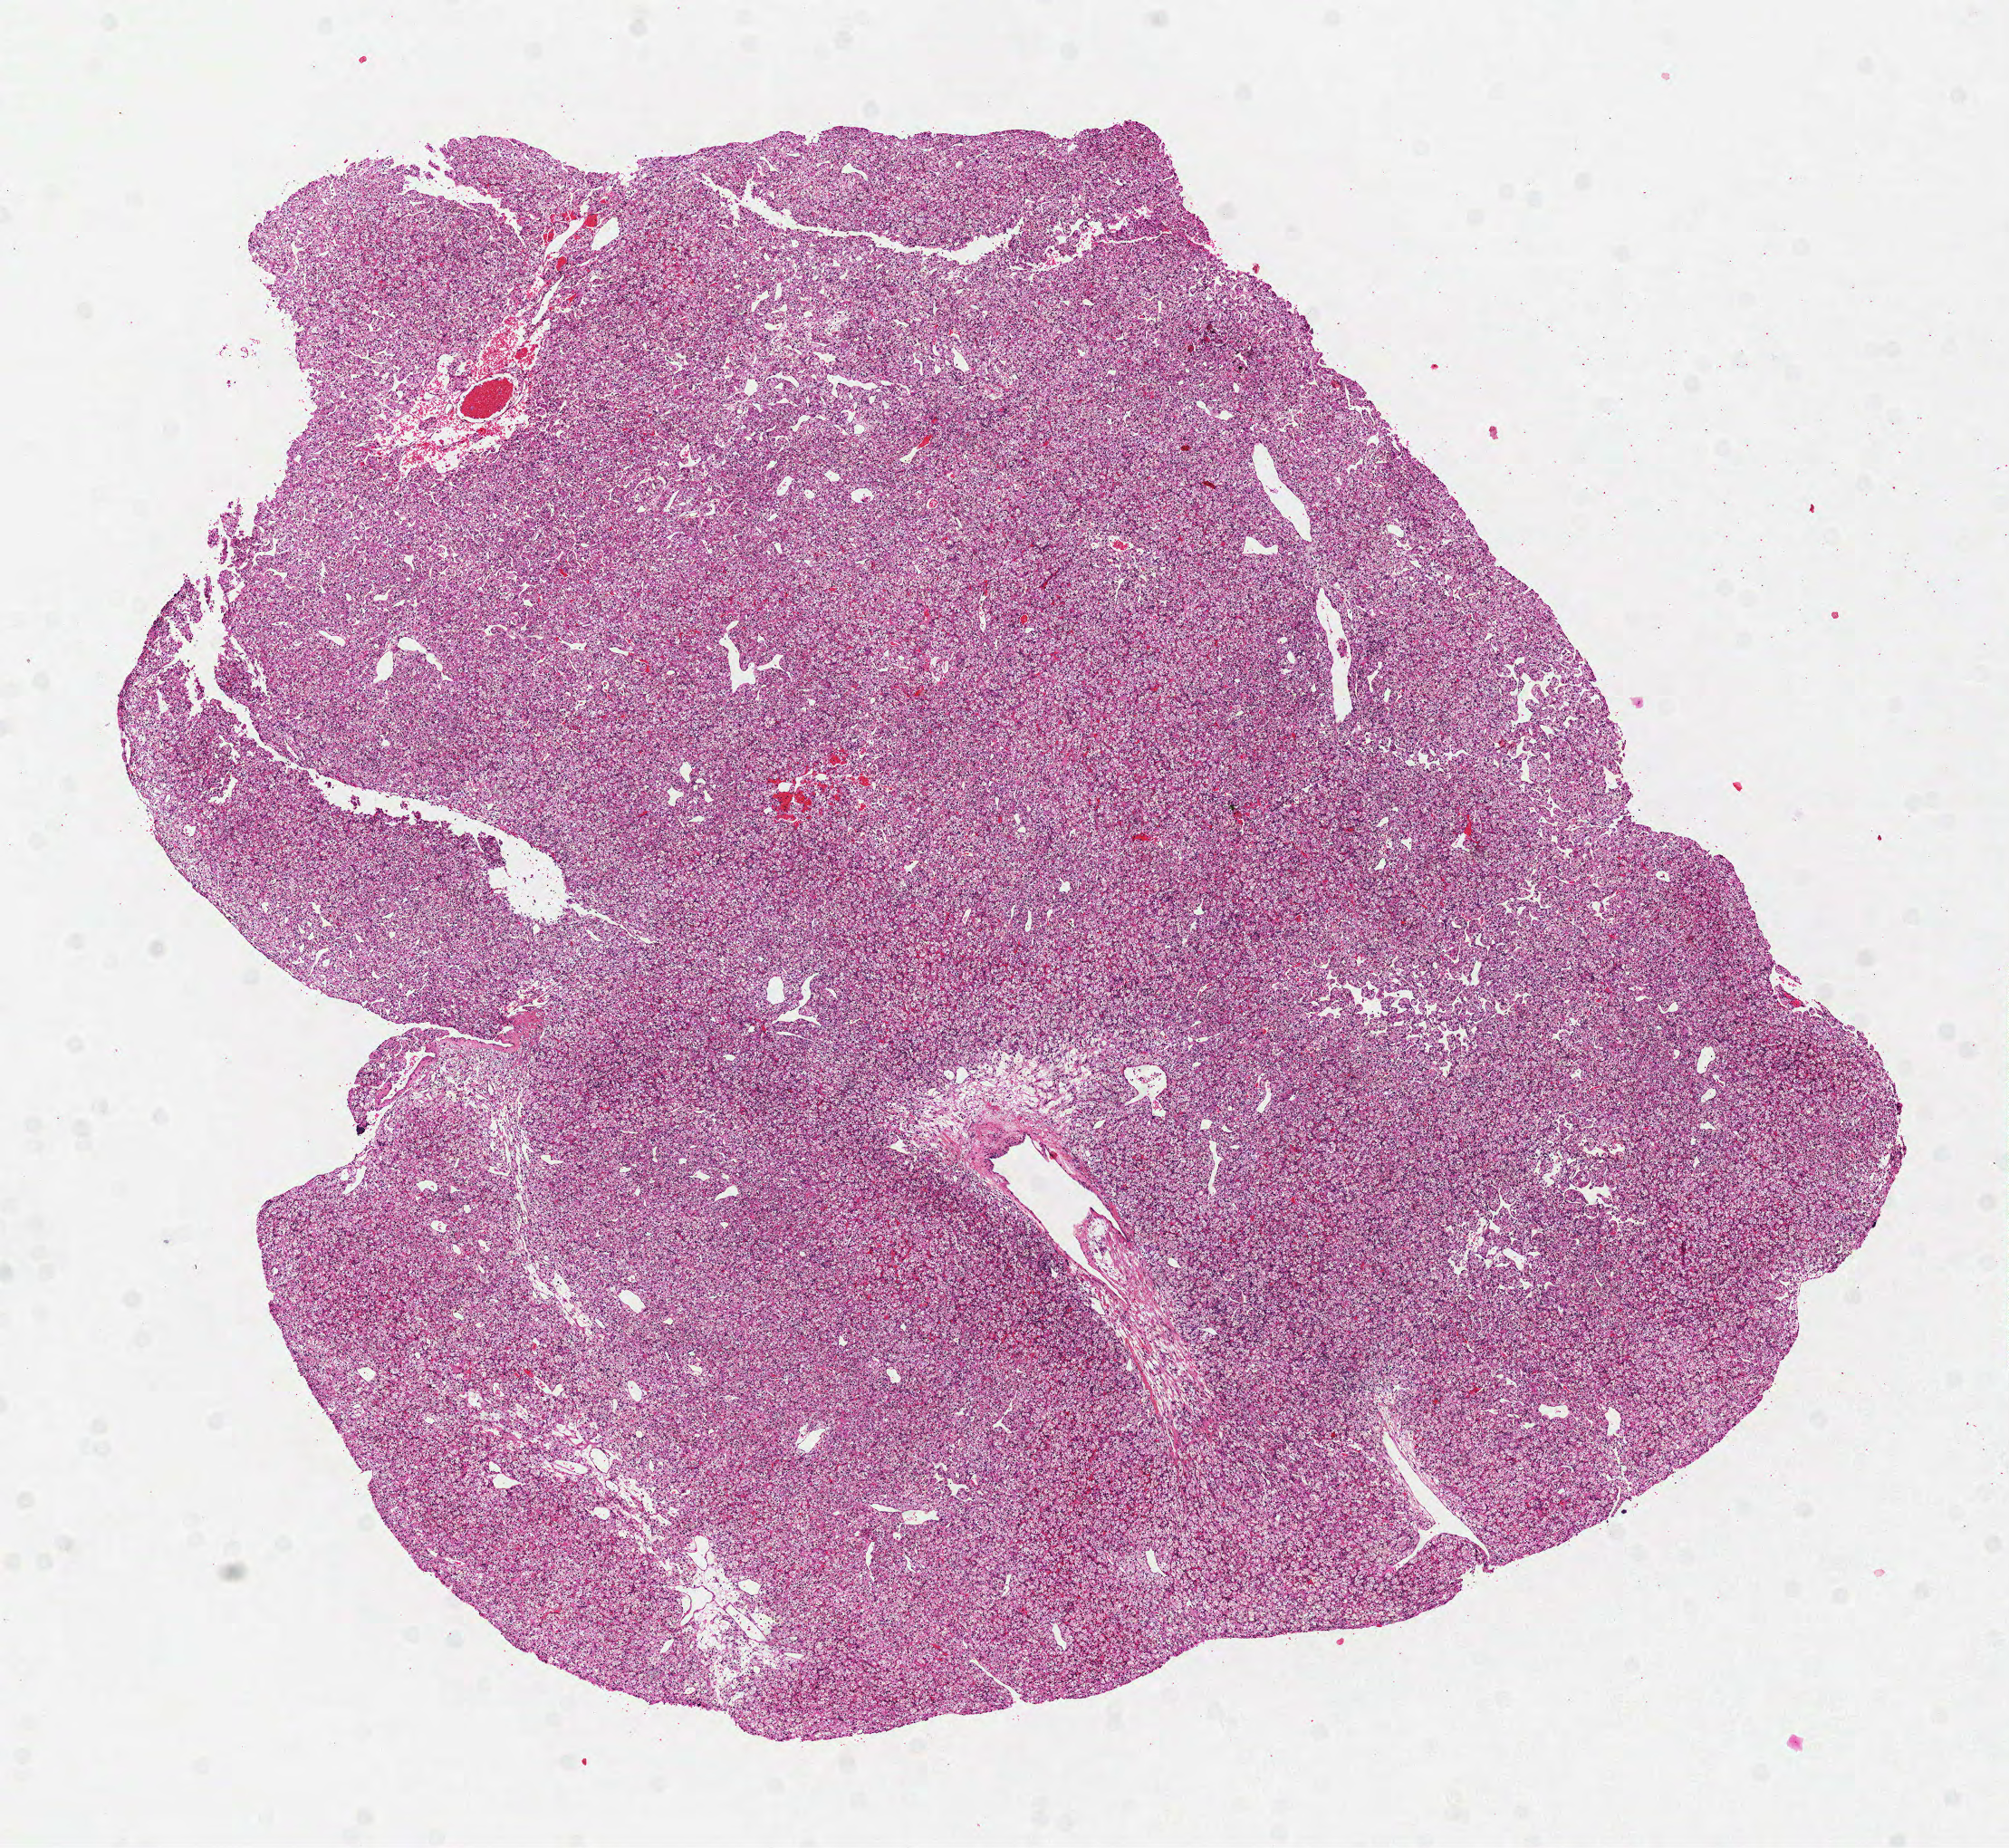
Whole-slide histology image, Hematoxylin and eosin (H&E) stained, low-resolution overview of the scanned area, about 8.9 x 8.2 mm (from a 40x scan). Formalin-fixed paraffin-embedded (FFPE) diagnostic section. Sample: primary tumour, kidney. Female, age 73 years at initial diagnosis.
Pathologic diagnosis: Clear cell adenocarcinoma, NOS.